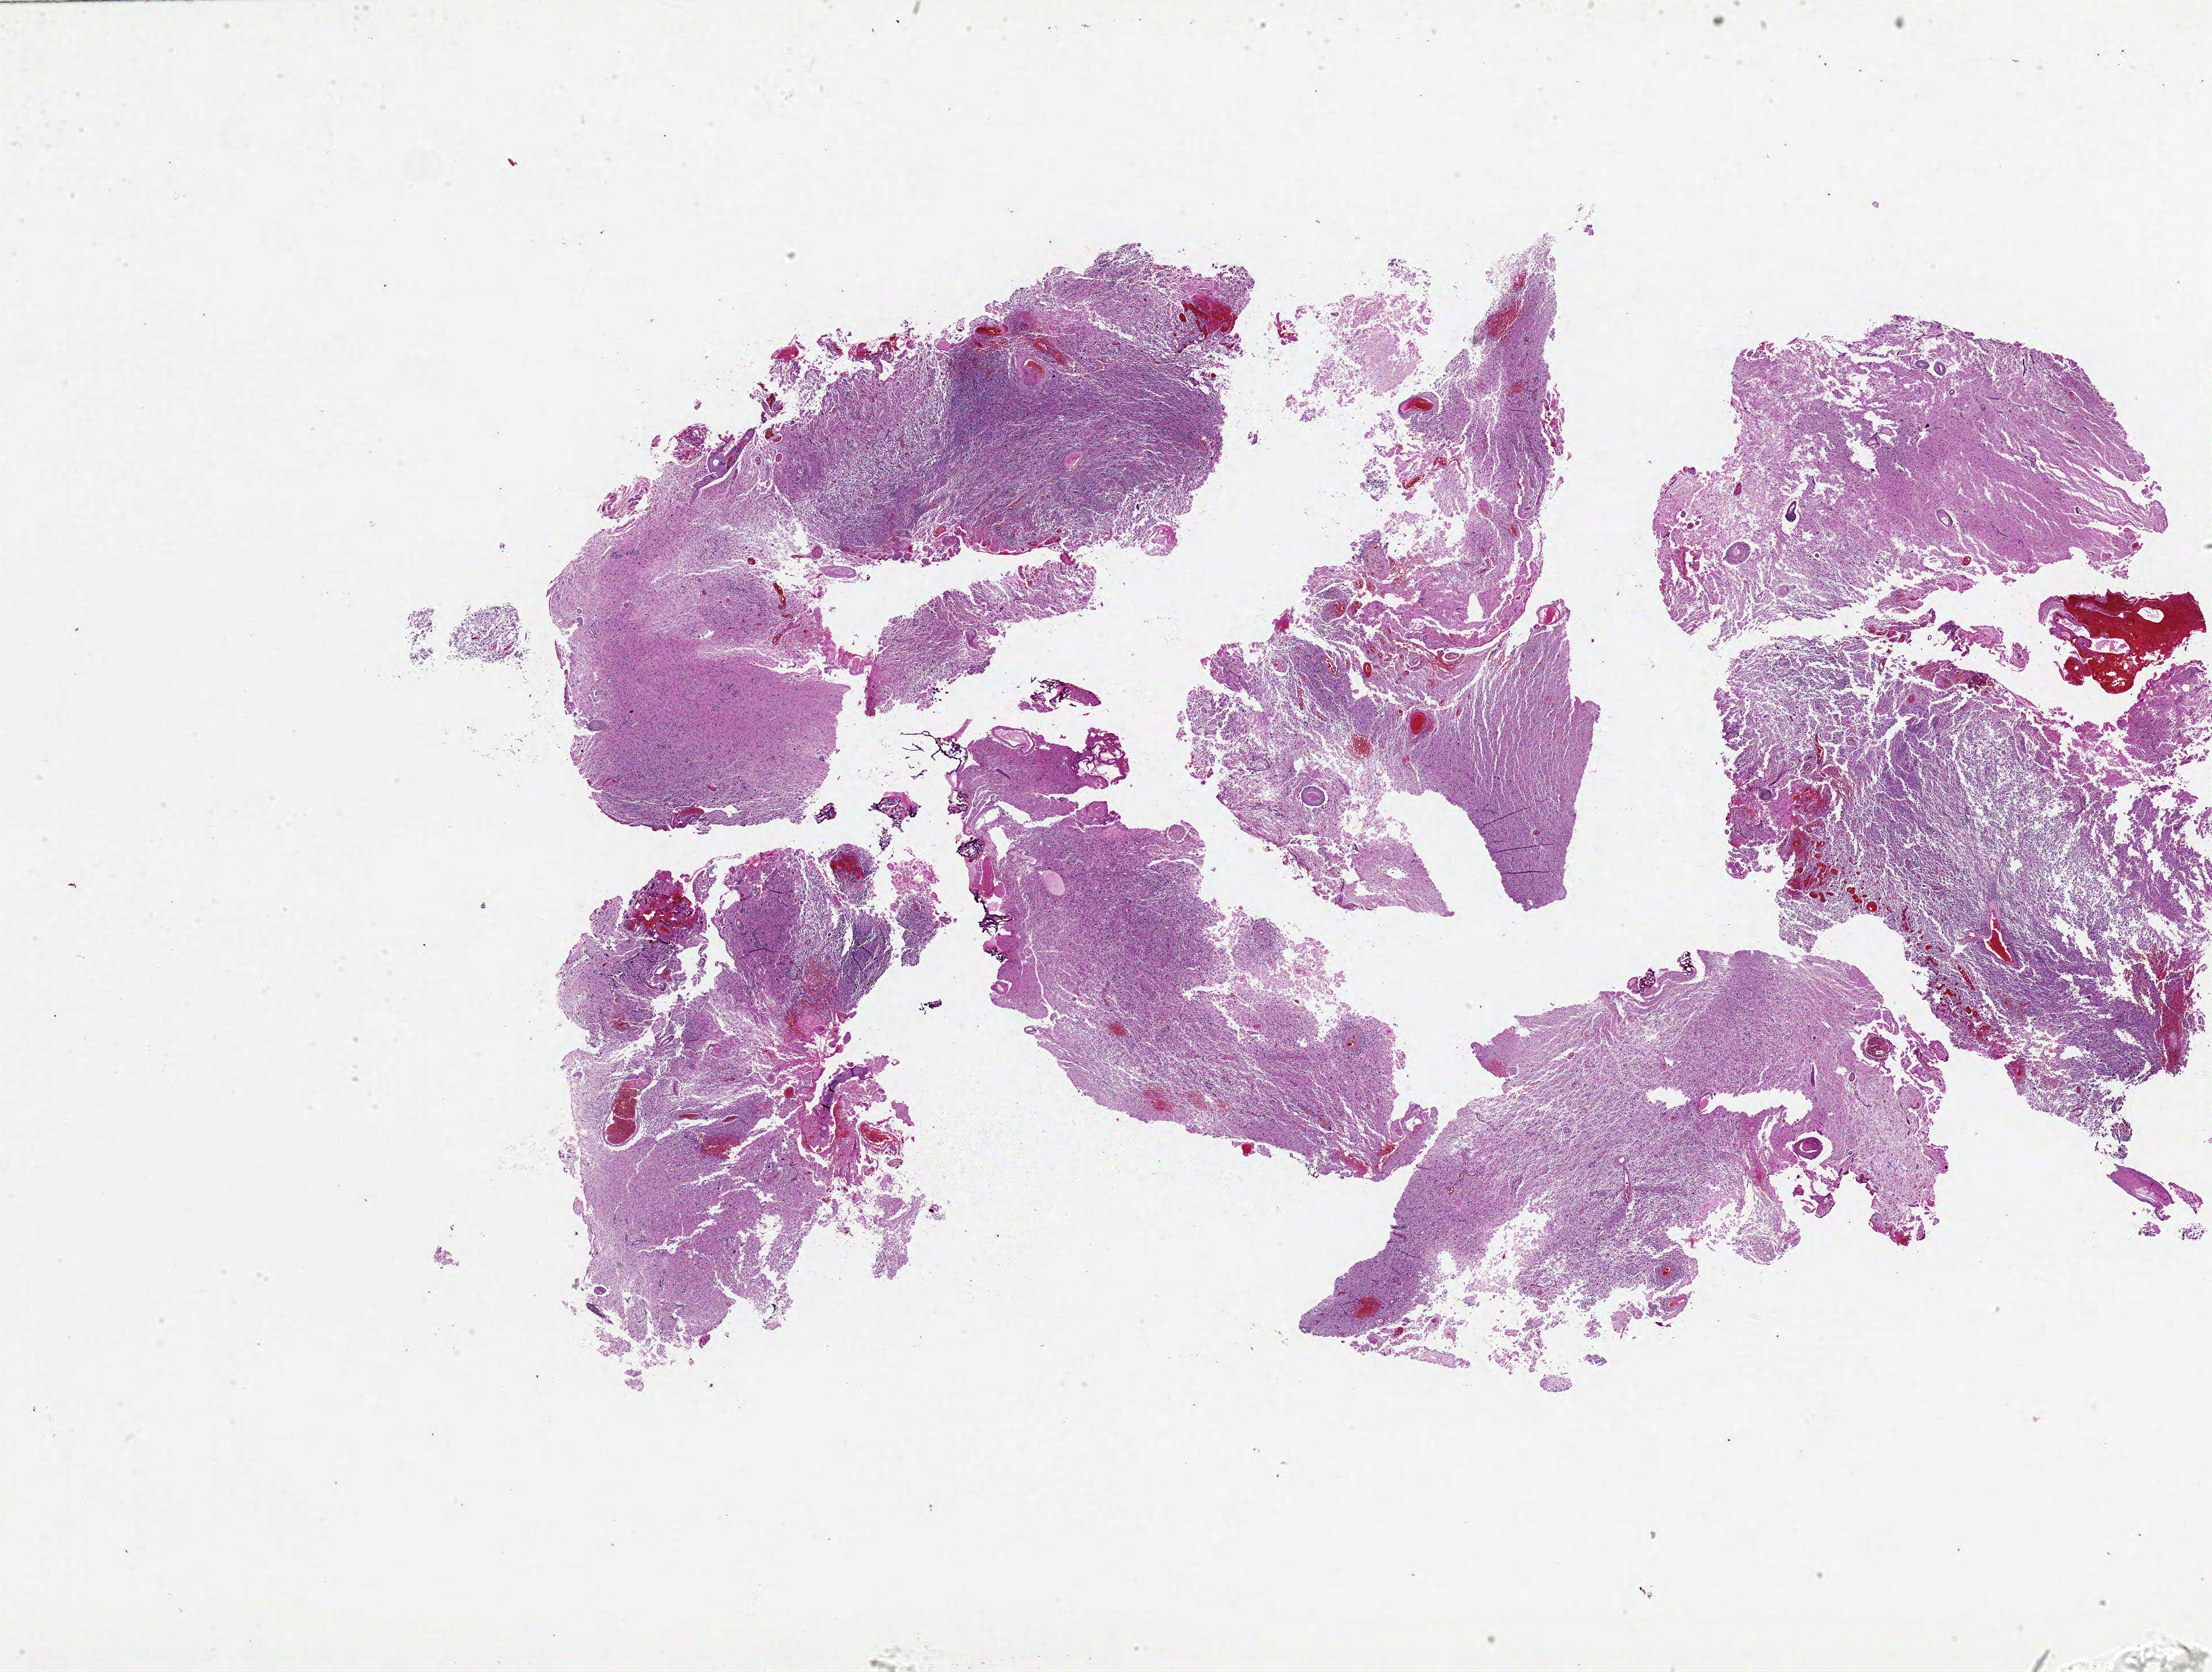
Whole-slide histology image, Hematoxylin and eosin (H&E) stained — a low-resolution overview of the entire scanned area, about 31.0 x 23.4 mm, formalin-fixed paraffin-embedded (FFPE) diagnostic section, primary tumour sample from the brain. Female patient; age at initial diagnosis 75 years.
- diagnosis: Glioblastoma